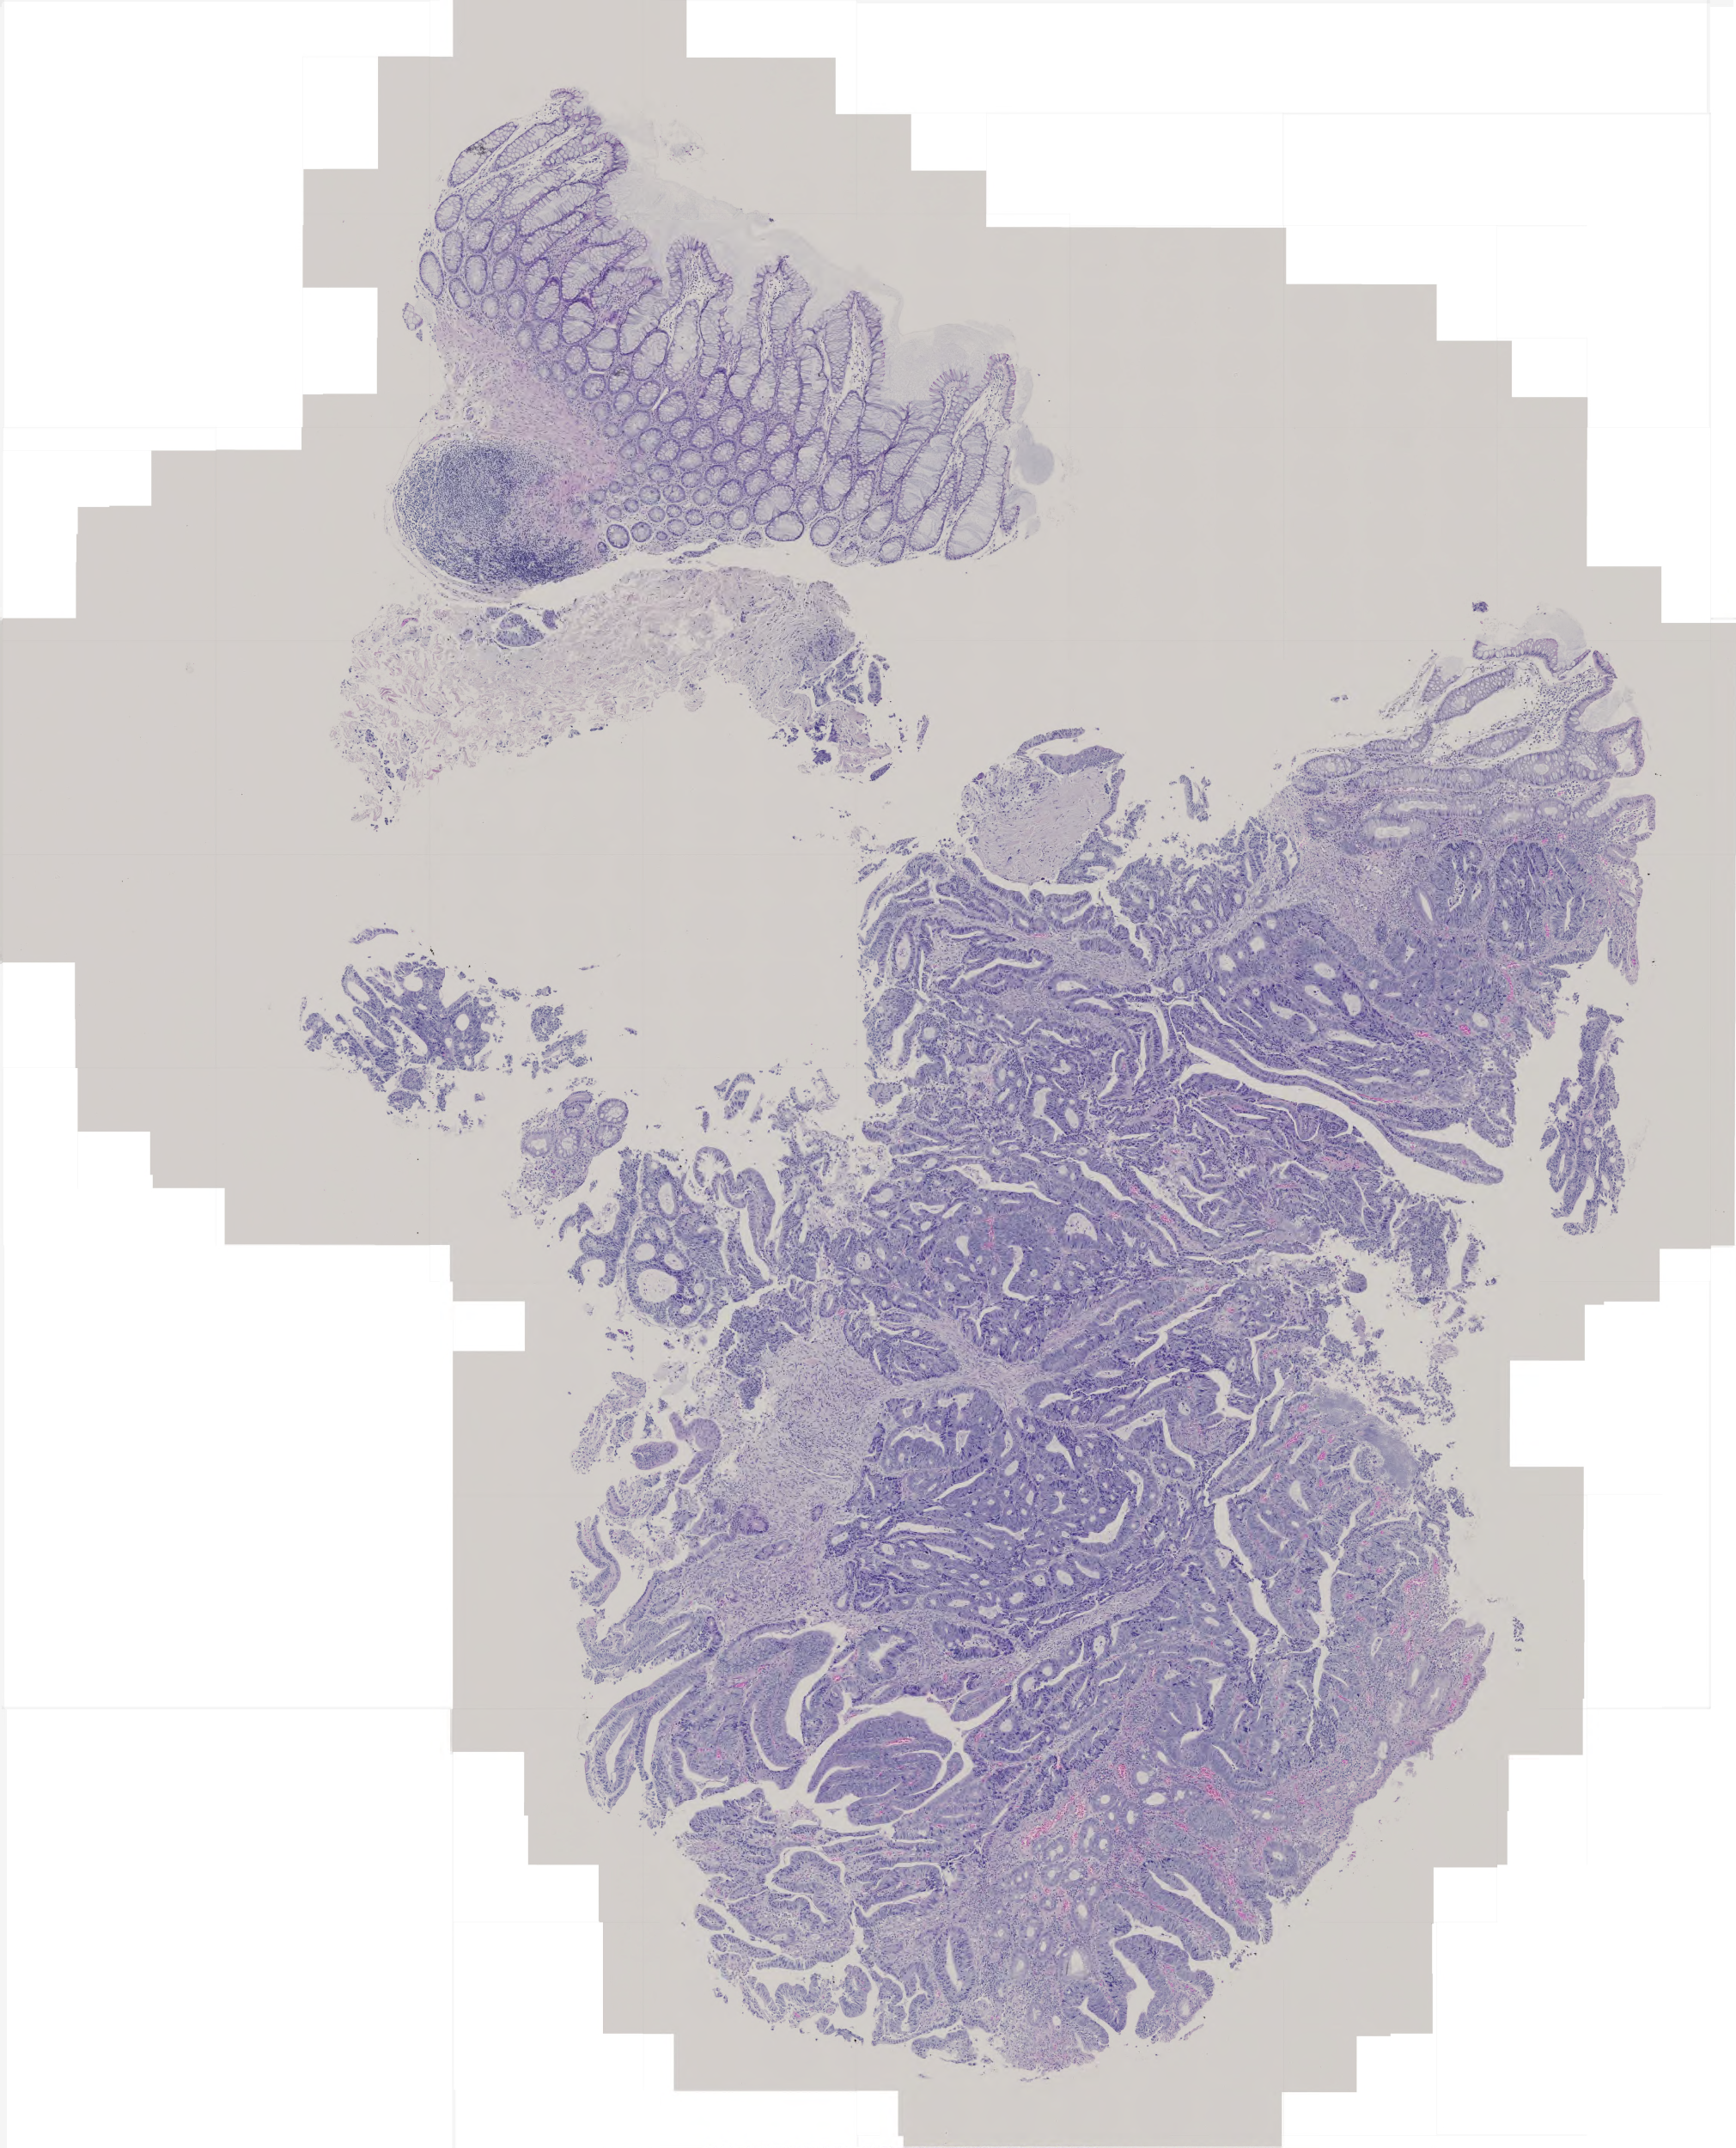
H&E-stained whole-slide image — shown as a low-resolution overview of the whole scanned area (about 4.0 x 5.0 mm); formalin-fixed paraffin-embedded (FFPE) diagnostic section; primary tumour sample from the colon. Male patient; age at initial diagnosis 55 years.
• lymph nodes positive (case pathology): 0 of 39 examined
• histologic diagnosis: Adenocarcinoma, NOS
• AJCC pathologic stage: IV (5th edition)
• TNM: T3 N0 M1